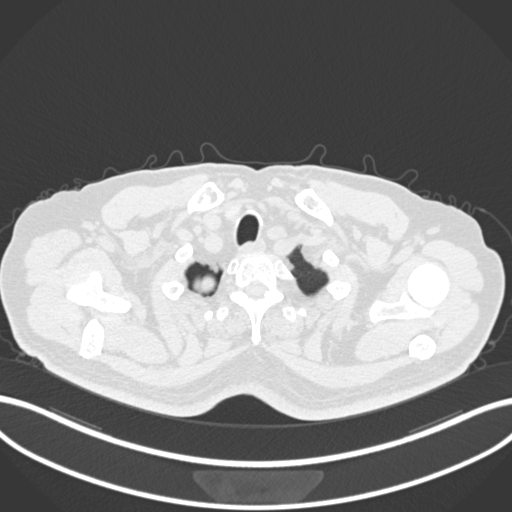
Chest CT, one axial slice; position 204 of 218 along the scan axis; reconstruction kernel B30f; lung window (W 1500 / L -600 HU); 1 mm slice thickness; 512 × 512 image matrix, field of view 400 × 400 mm. Male patient, age 68 years. From the clinical record (not read from this slice): clinical TNM (as recorded): T2a N0 M0.
Annotated regions visible in this slice (bounding box drawn by a radiologist):
- lung tumour (recorded histology: adenocarcinoma): box from (x=192, y=271) to (x=217, y=297) px